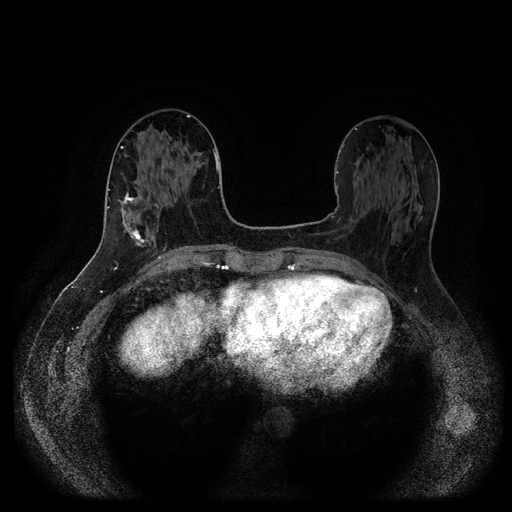
Breast MRI (dynamic contrast-enhanced, multi-phase), one axial slice. Slice 43 of 116 in the series (ordered by position). Dynamic contrast-enhanced series, time point 2 of 5 at this slice position (early post-contrast). 1.5 T. TE 2.6 ms, TR 5.3 ms. 2 mm slice thickness. 512 × 512 image matrix, field of view 360 × 360 mm. Patient: female, 58 years.
Annotated regions visible in this slice (semi-automatically segmented with operator editing):
- breast lesion (labelled 'tumour' in the annotation; benign lesions carry a separate 'benign' label): bounding box (x1, y1, x2, y2) in pixels: (121, 189, 148, 248)